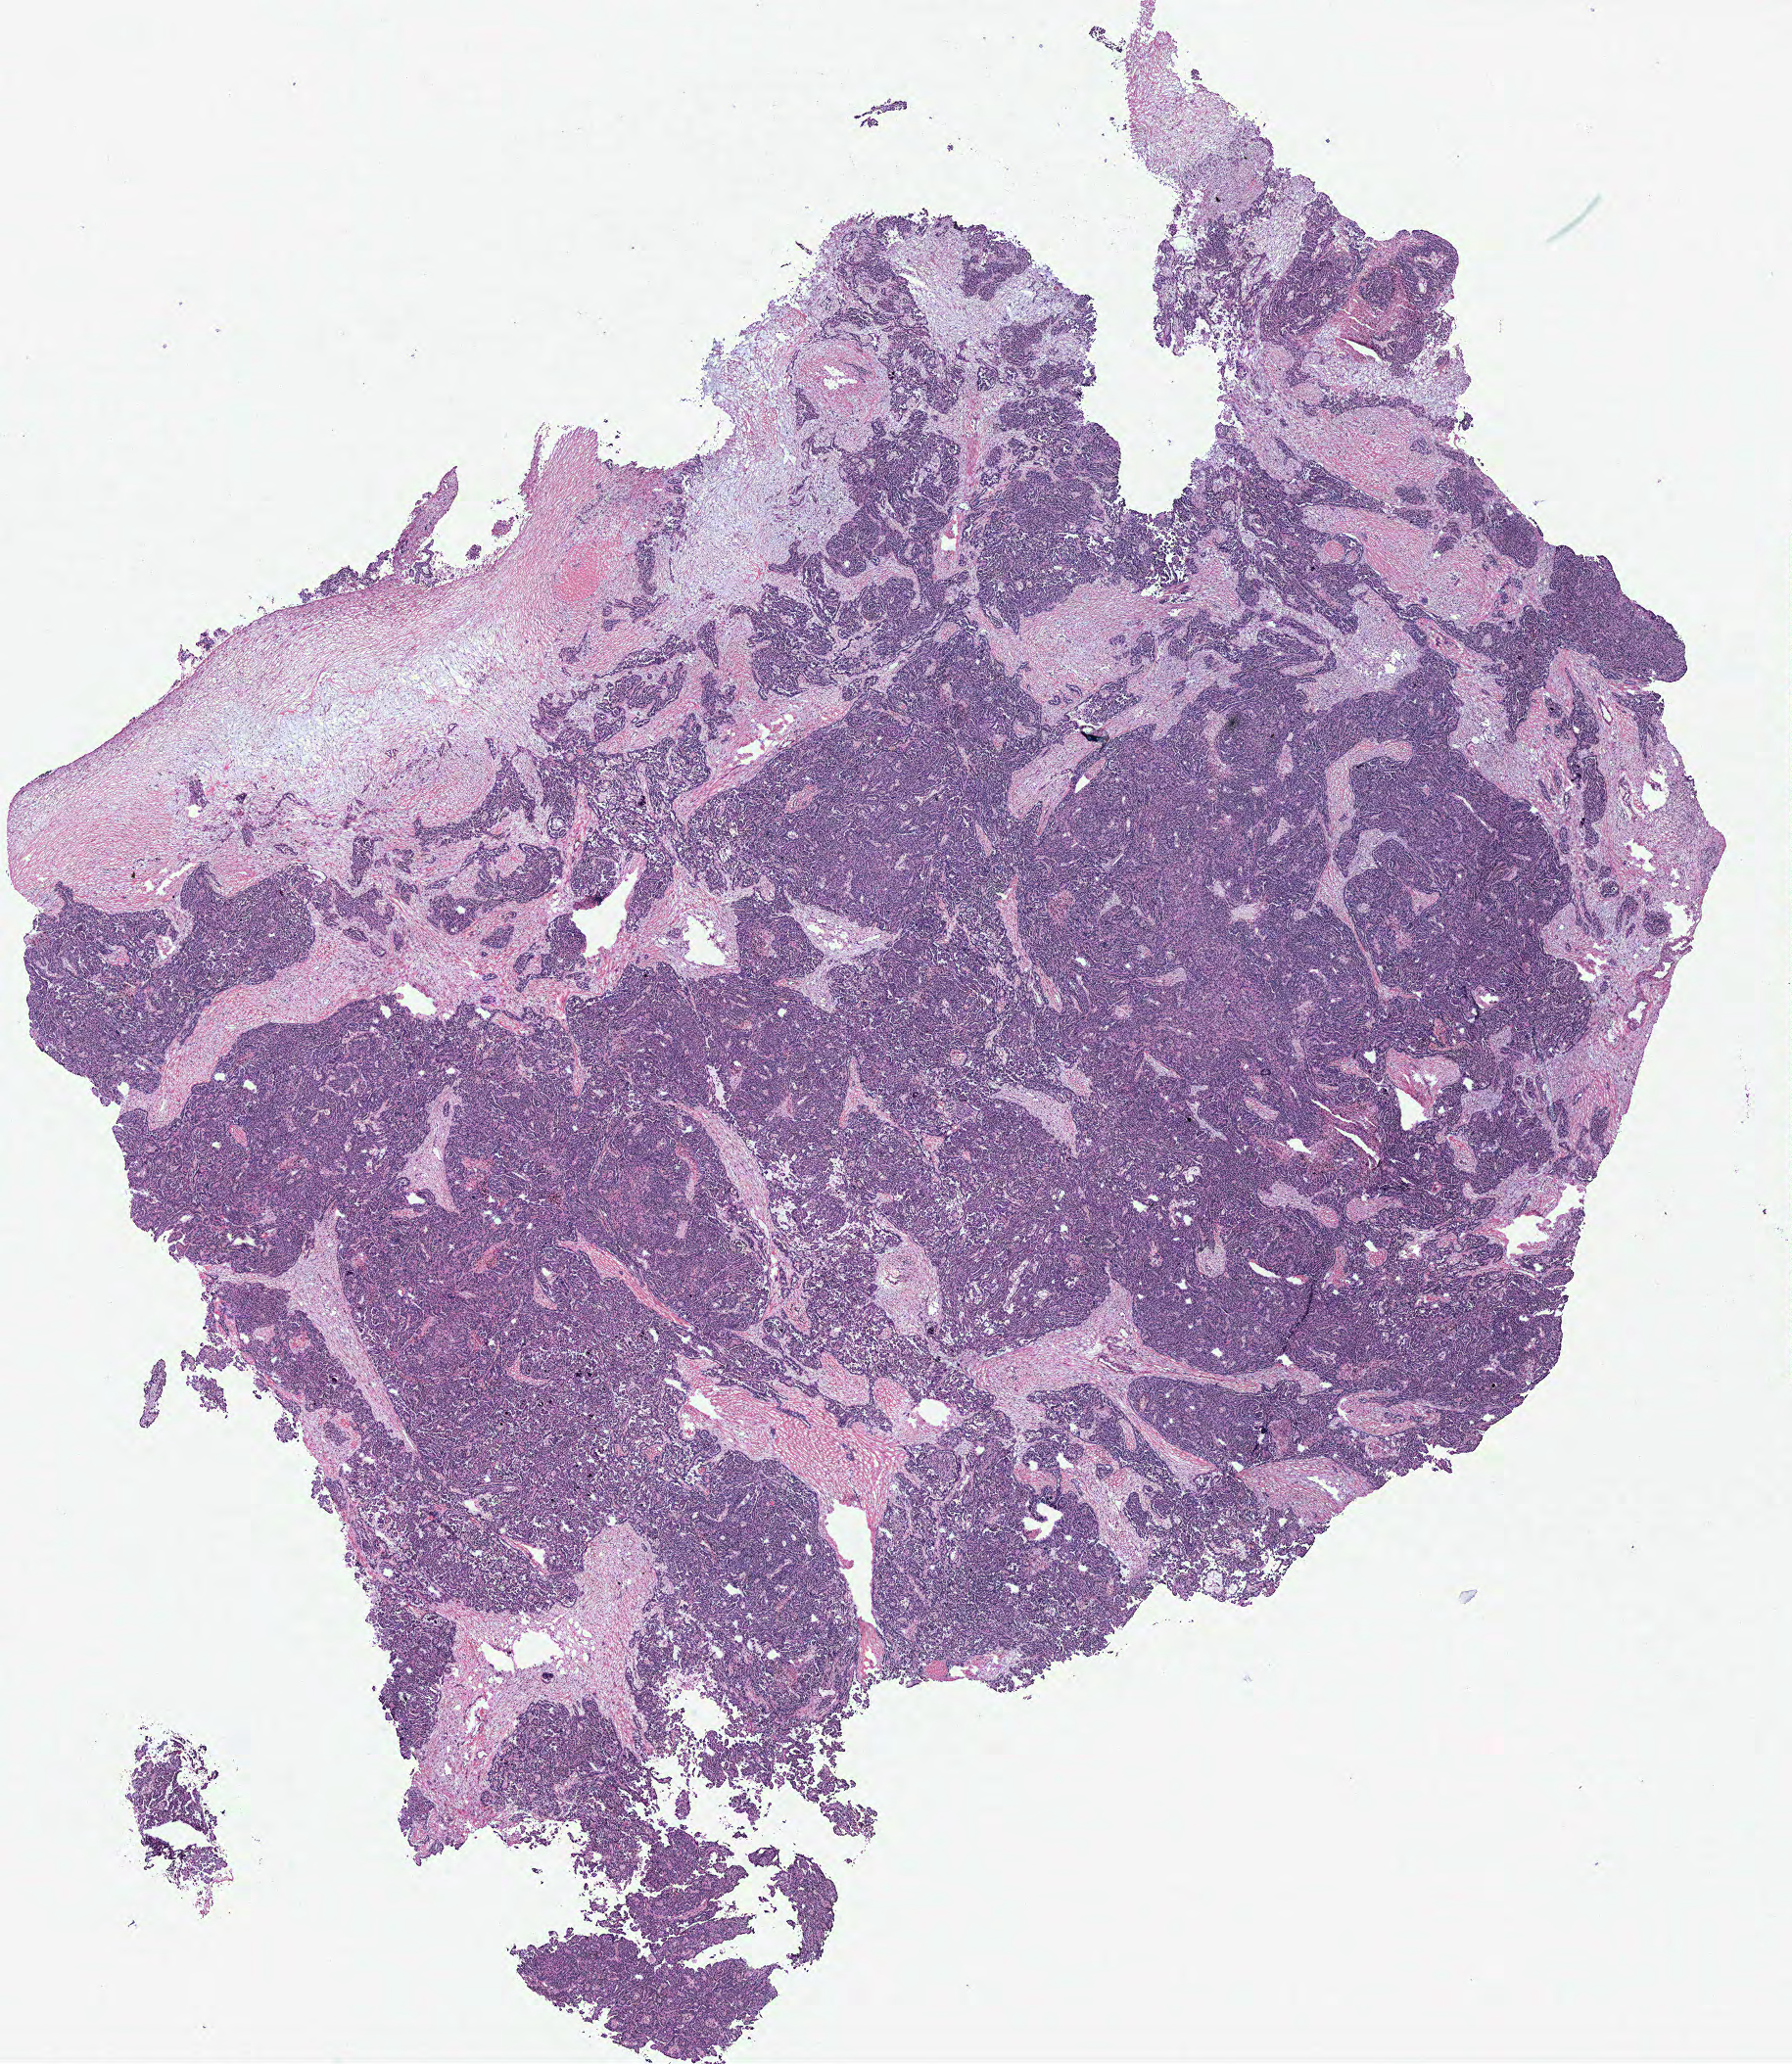
H&E-stained whole-slide image, whole scanned area (about 14.6 x 16.9 mm, slide scanned at 40x) shown as a low-resolution overview. Ovary, tumour tissue. Patient: female, age 65 years.
• primary tumour site (as recorded): ovary
• histologic diagnosis: Serous adenocarcinoma, NOS